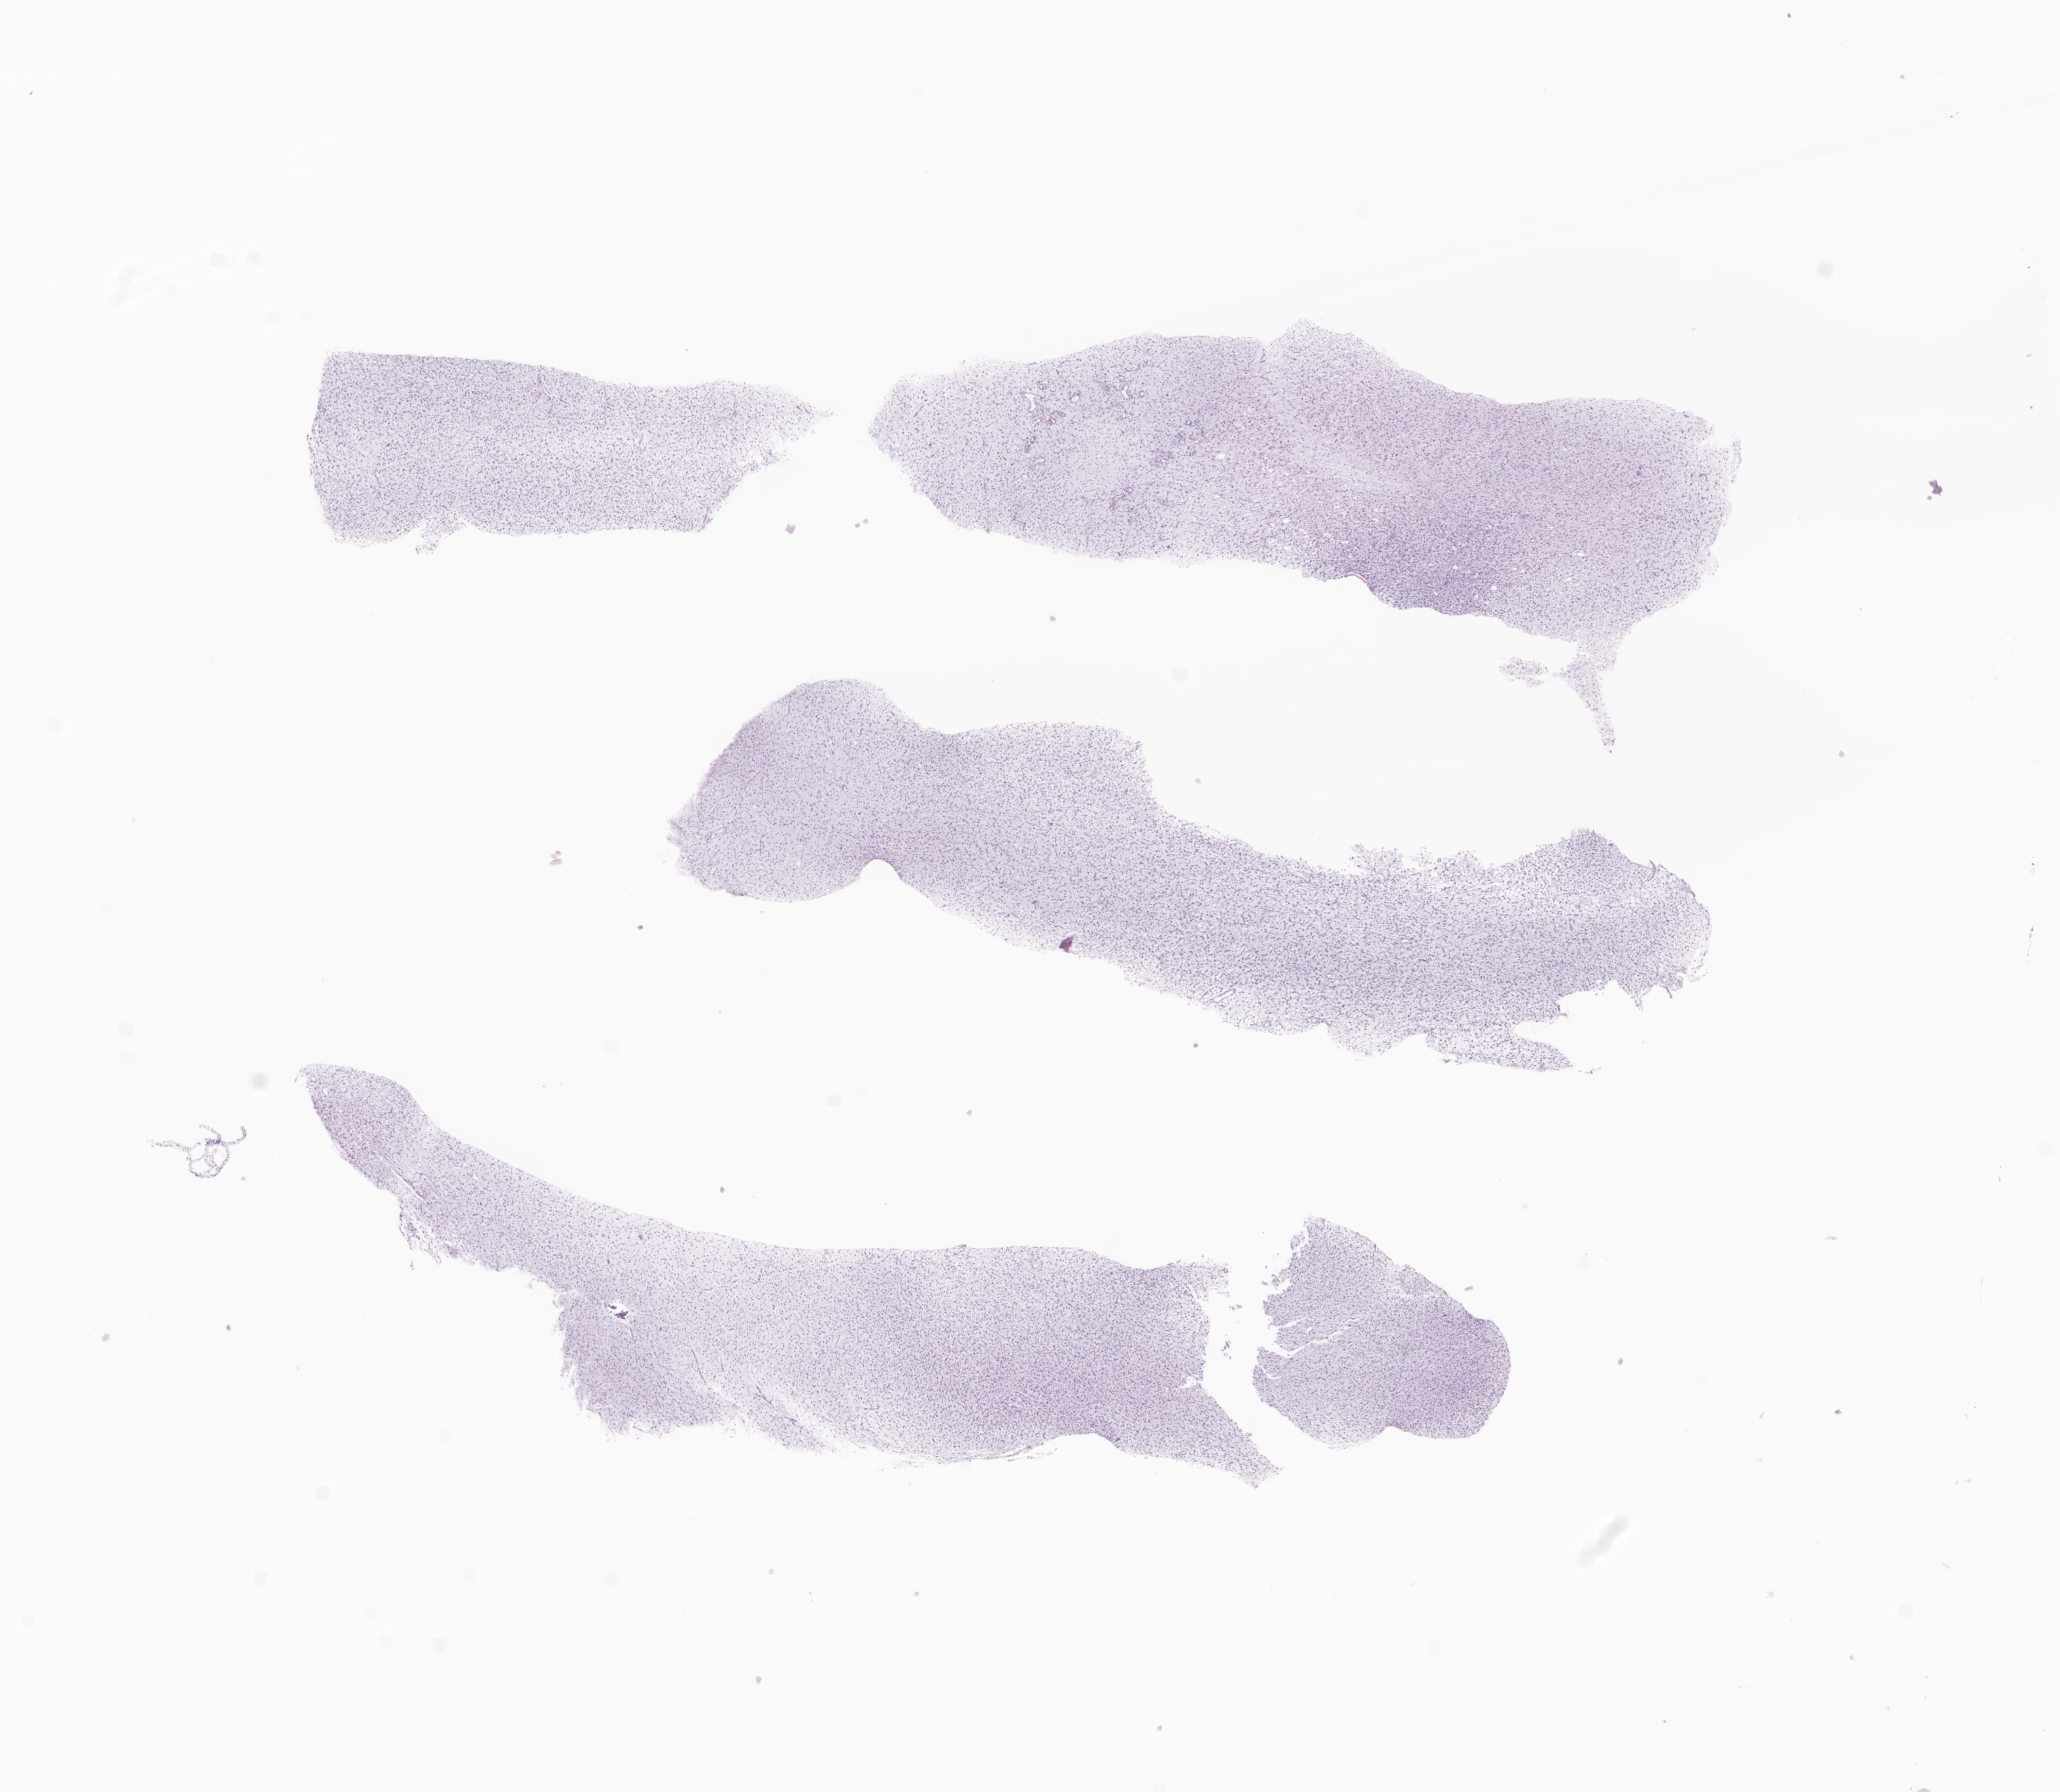
H&E whole-slide image of tumor tissue from the brain — shown as a low-resolution overview of the whole scanned area (about 12.8 x 11.1 mm). Formalin-fixed paraffin-embedded section. Patient: female, age 73 months.
• recorded diagnosis: Glioma, malignant